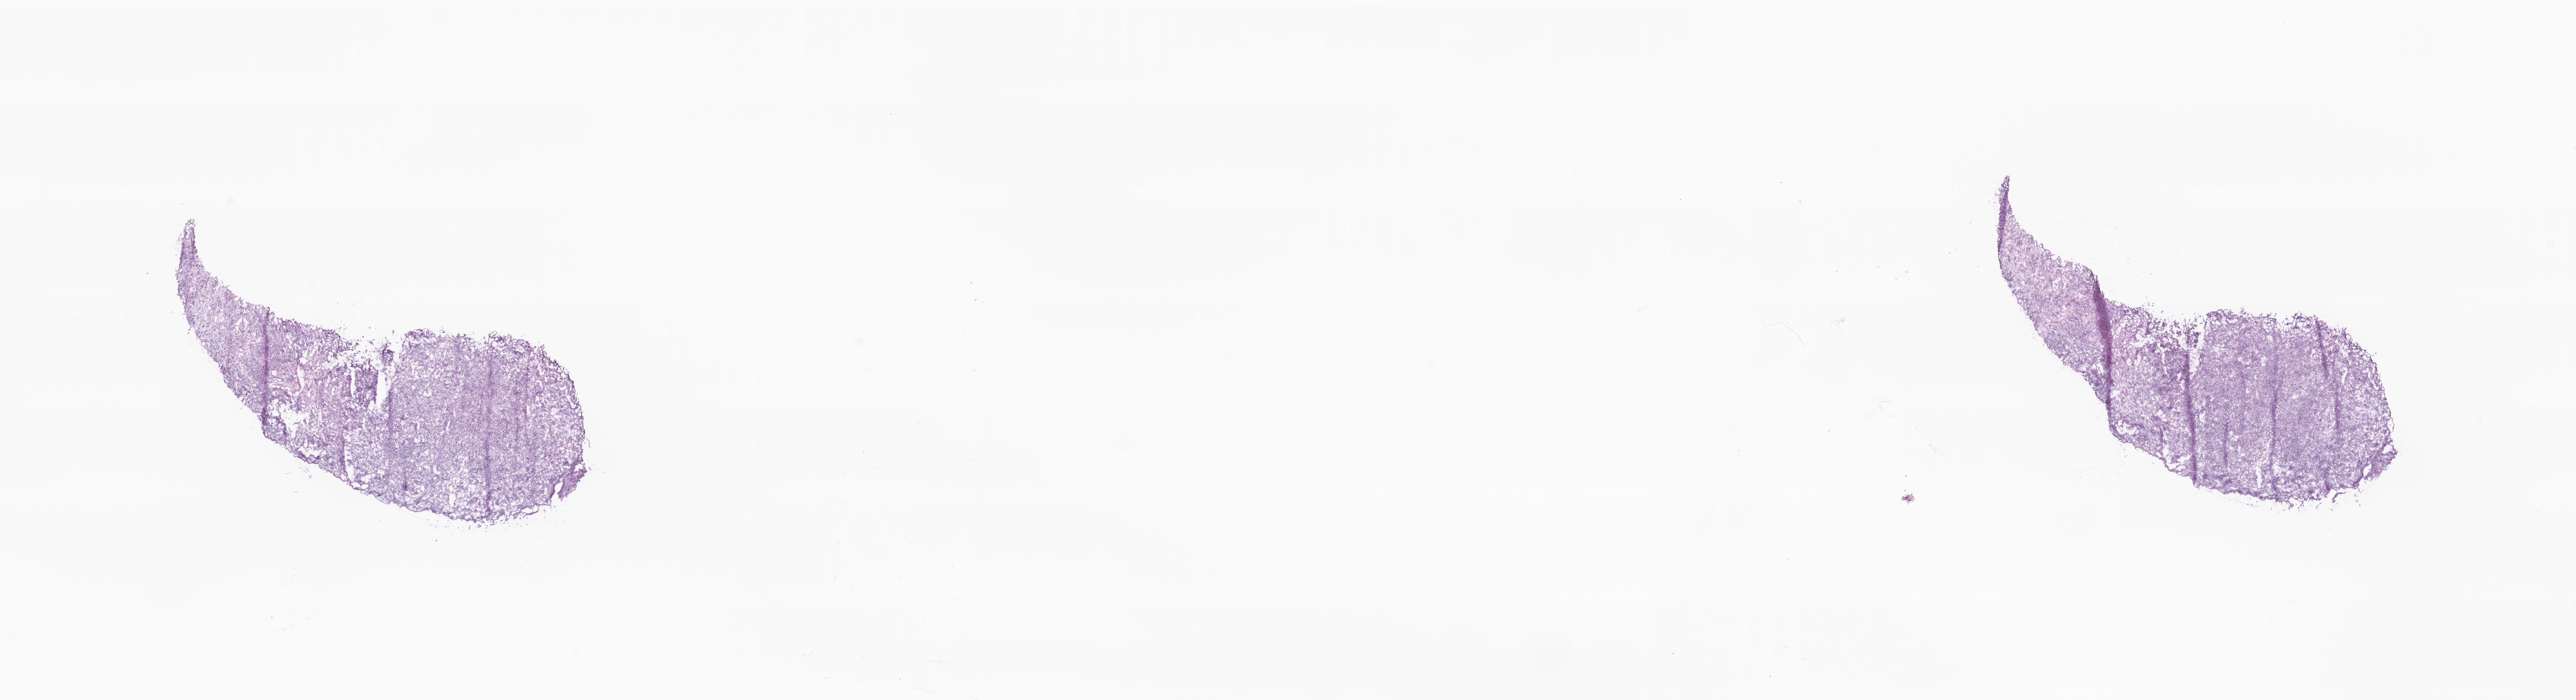
Digitized haematoxylin and eosin-stained section — a low-resolution overview of the entire scanned area, about 27.3 x 7.4 mm, cryosection, specimen: metastatic tumor tissue. Patient: male, age at initial diagnosis 82 years. Composition of this section per pathologist review: tumor cells 100%, tumor nuclei 80%, stromal cells 0%, necrosis 0%, normal cells 0%. Inflammatory infiltration, as recorded: lymphocyte infiltration 0%, monocyte infiltration 0%, neutrophil infiltration 0%.
- patient diagnosis (primary): Adenocarcinoma, NOS